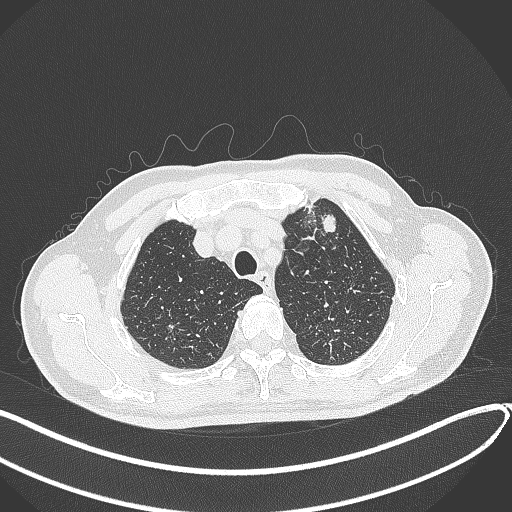
Chest CT, one axial slice; position 354 of 459 along the scan axis; 120 kVp; lung window (W 1500 / L -600 HU); 1 mm slice thickness; 512 × 512 image matrix, field of view 400 × 400 mm. Patient: male, 74 years. Case-level facts recorded for this patient, not image findings: clinical TNM (as recorded): T2b N0 M1c.
Annotated regions visible in this slice (bounding box drawn by a radiologist):
- lung tumour (recorded histology: adenocarcinoma): bounding box [x1, y1, x2, y2] px = [315, 211, 339, 237]